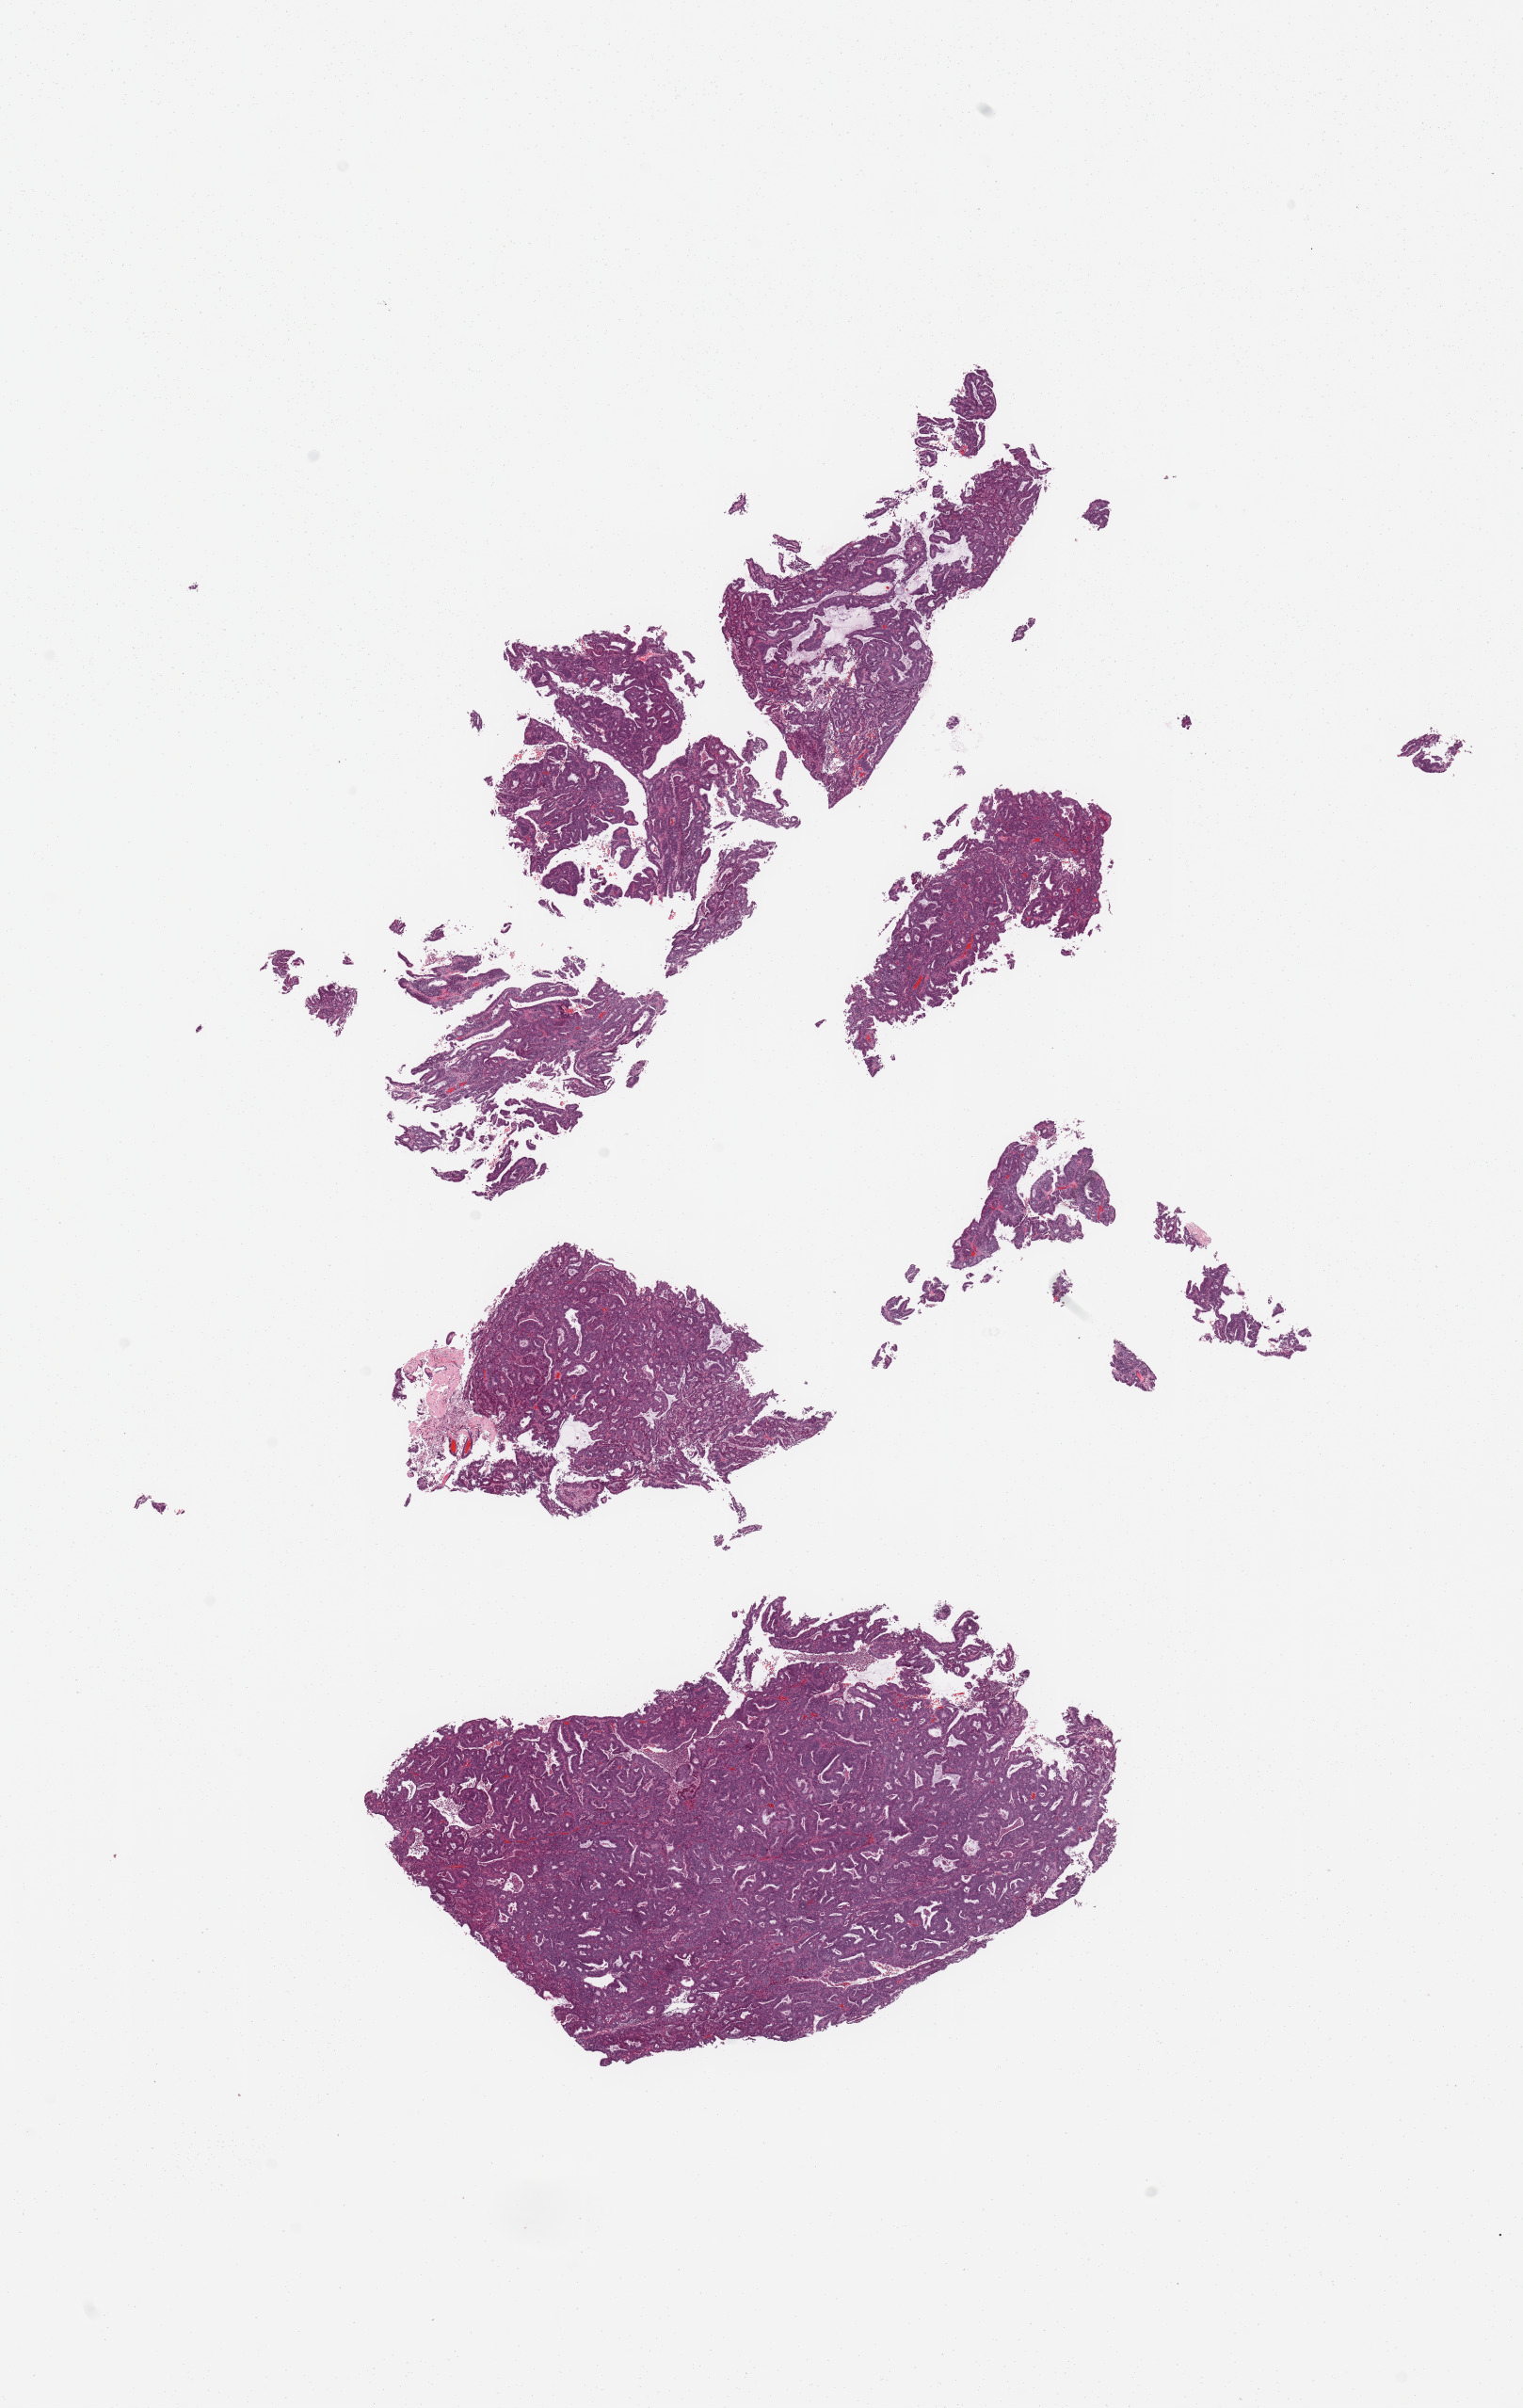
H&E-stained whole-slide image, shown as a low-resolution overview of the whole scanned area (about 12.8 x 20.2 mm), tumour tissue sample, sampled site: uterus. Female, 75 y/o. Histologic grade: G2 (moderately differentiated). Slide review estimates, as recorded: tumour nuclei 95%, necrosis 2%.
AJCC pathologic stage: I. Diagnosis: Endometrioid adenocarcinoma, NOS. Primary tumour site (as recorded): anterior endometrium.